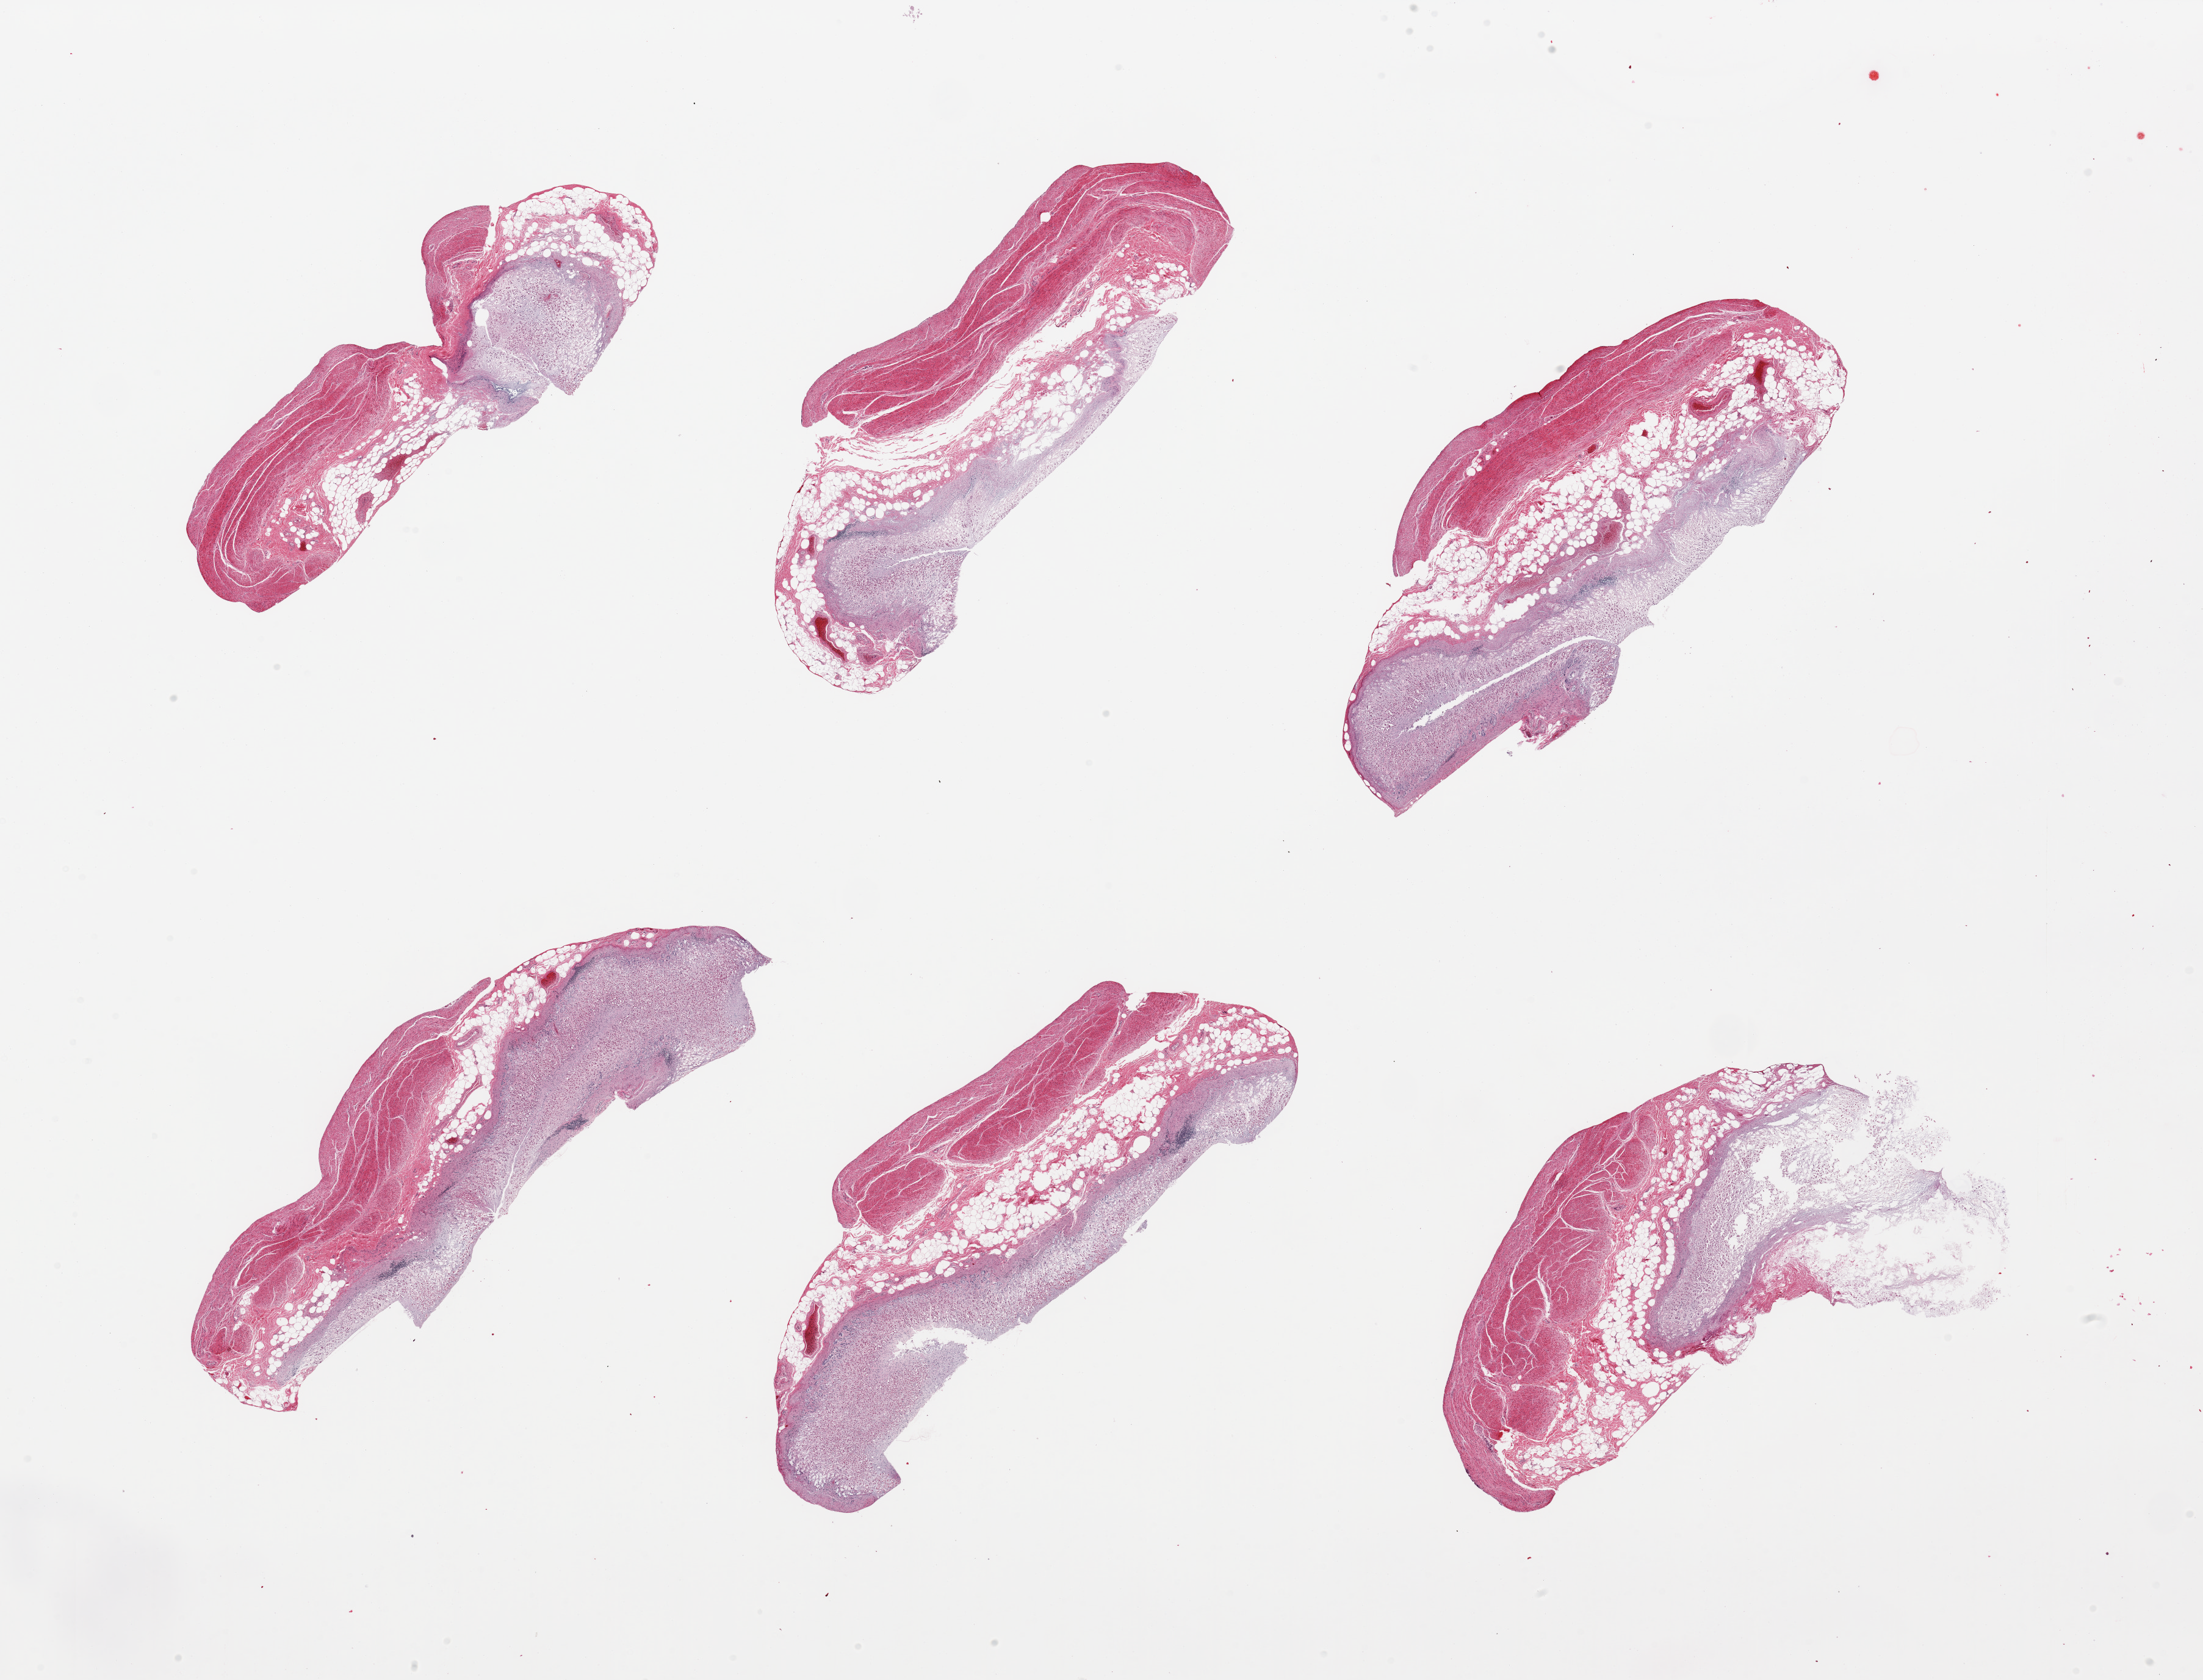
Hematoxylin and eosin (H&E) whole-slide image, brightfield, low-resolution overview of the scanned area, about 28.5 x 21.8 mm (from a 20x scan). Female donor.
- specimen: PAXgene-fixed, paraffin-embedded tissue; section of stomach (target tissue); donor tissue sample